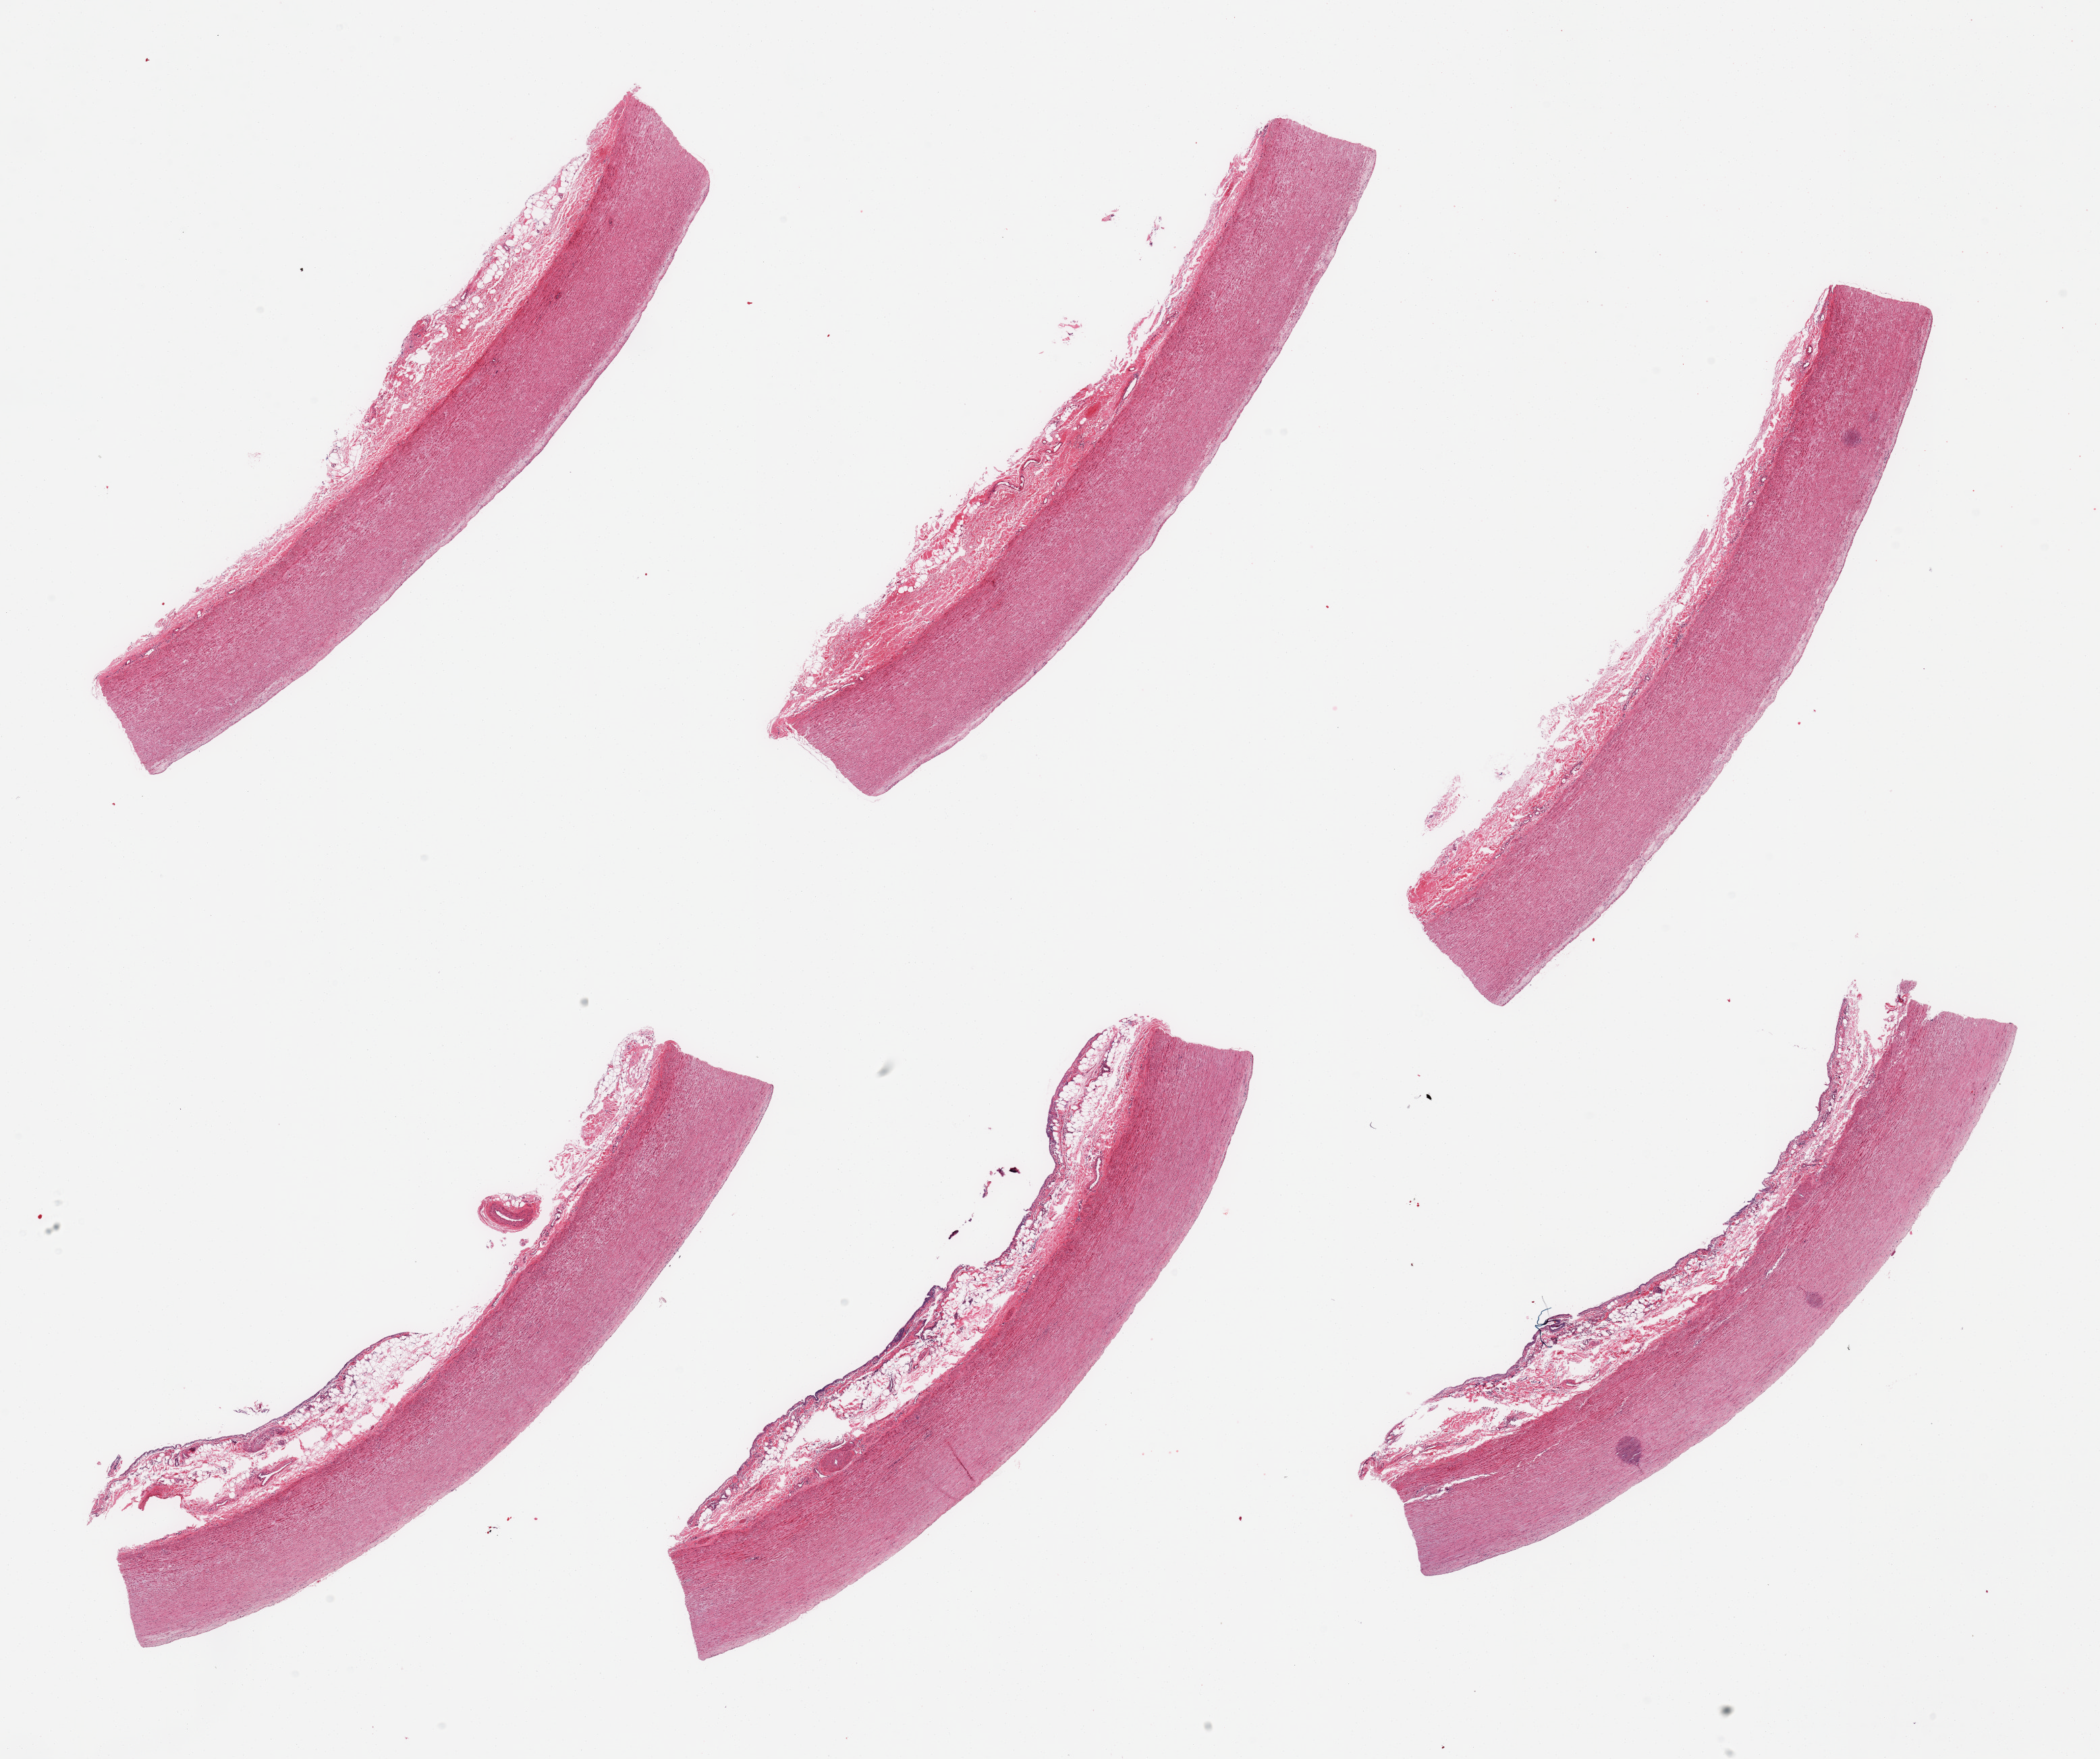
Haematoxylin and eosin whole-slide image, whole scanned area (about 24.6 x 20.6 mm) shown as a low-resolution overview; PAXgene-fixed, paraffin-embedded tissue; section of aorta (target tissue); donor tissue sample. Donor sex: male.
Reviewer comment on this tissue sample: 6 pieces; minimal plaque.